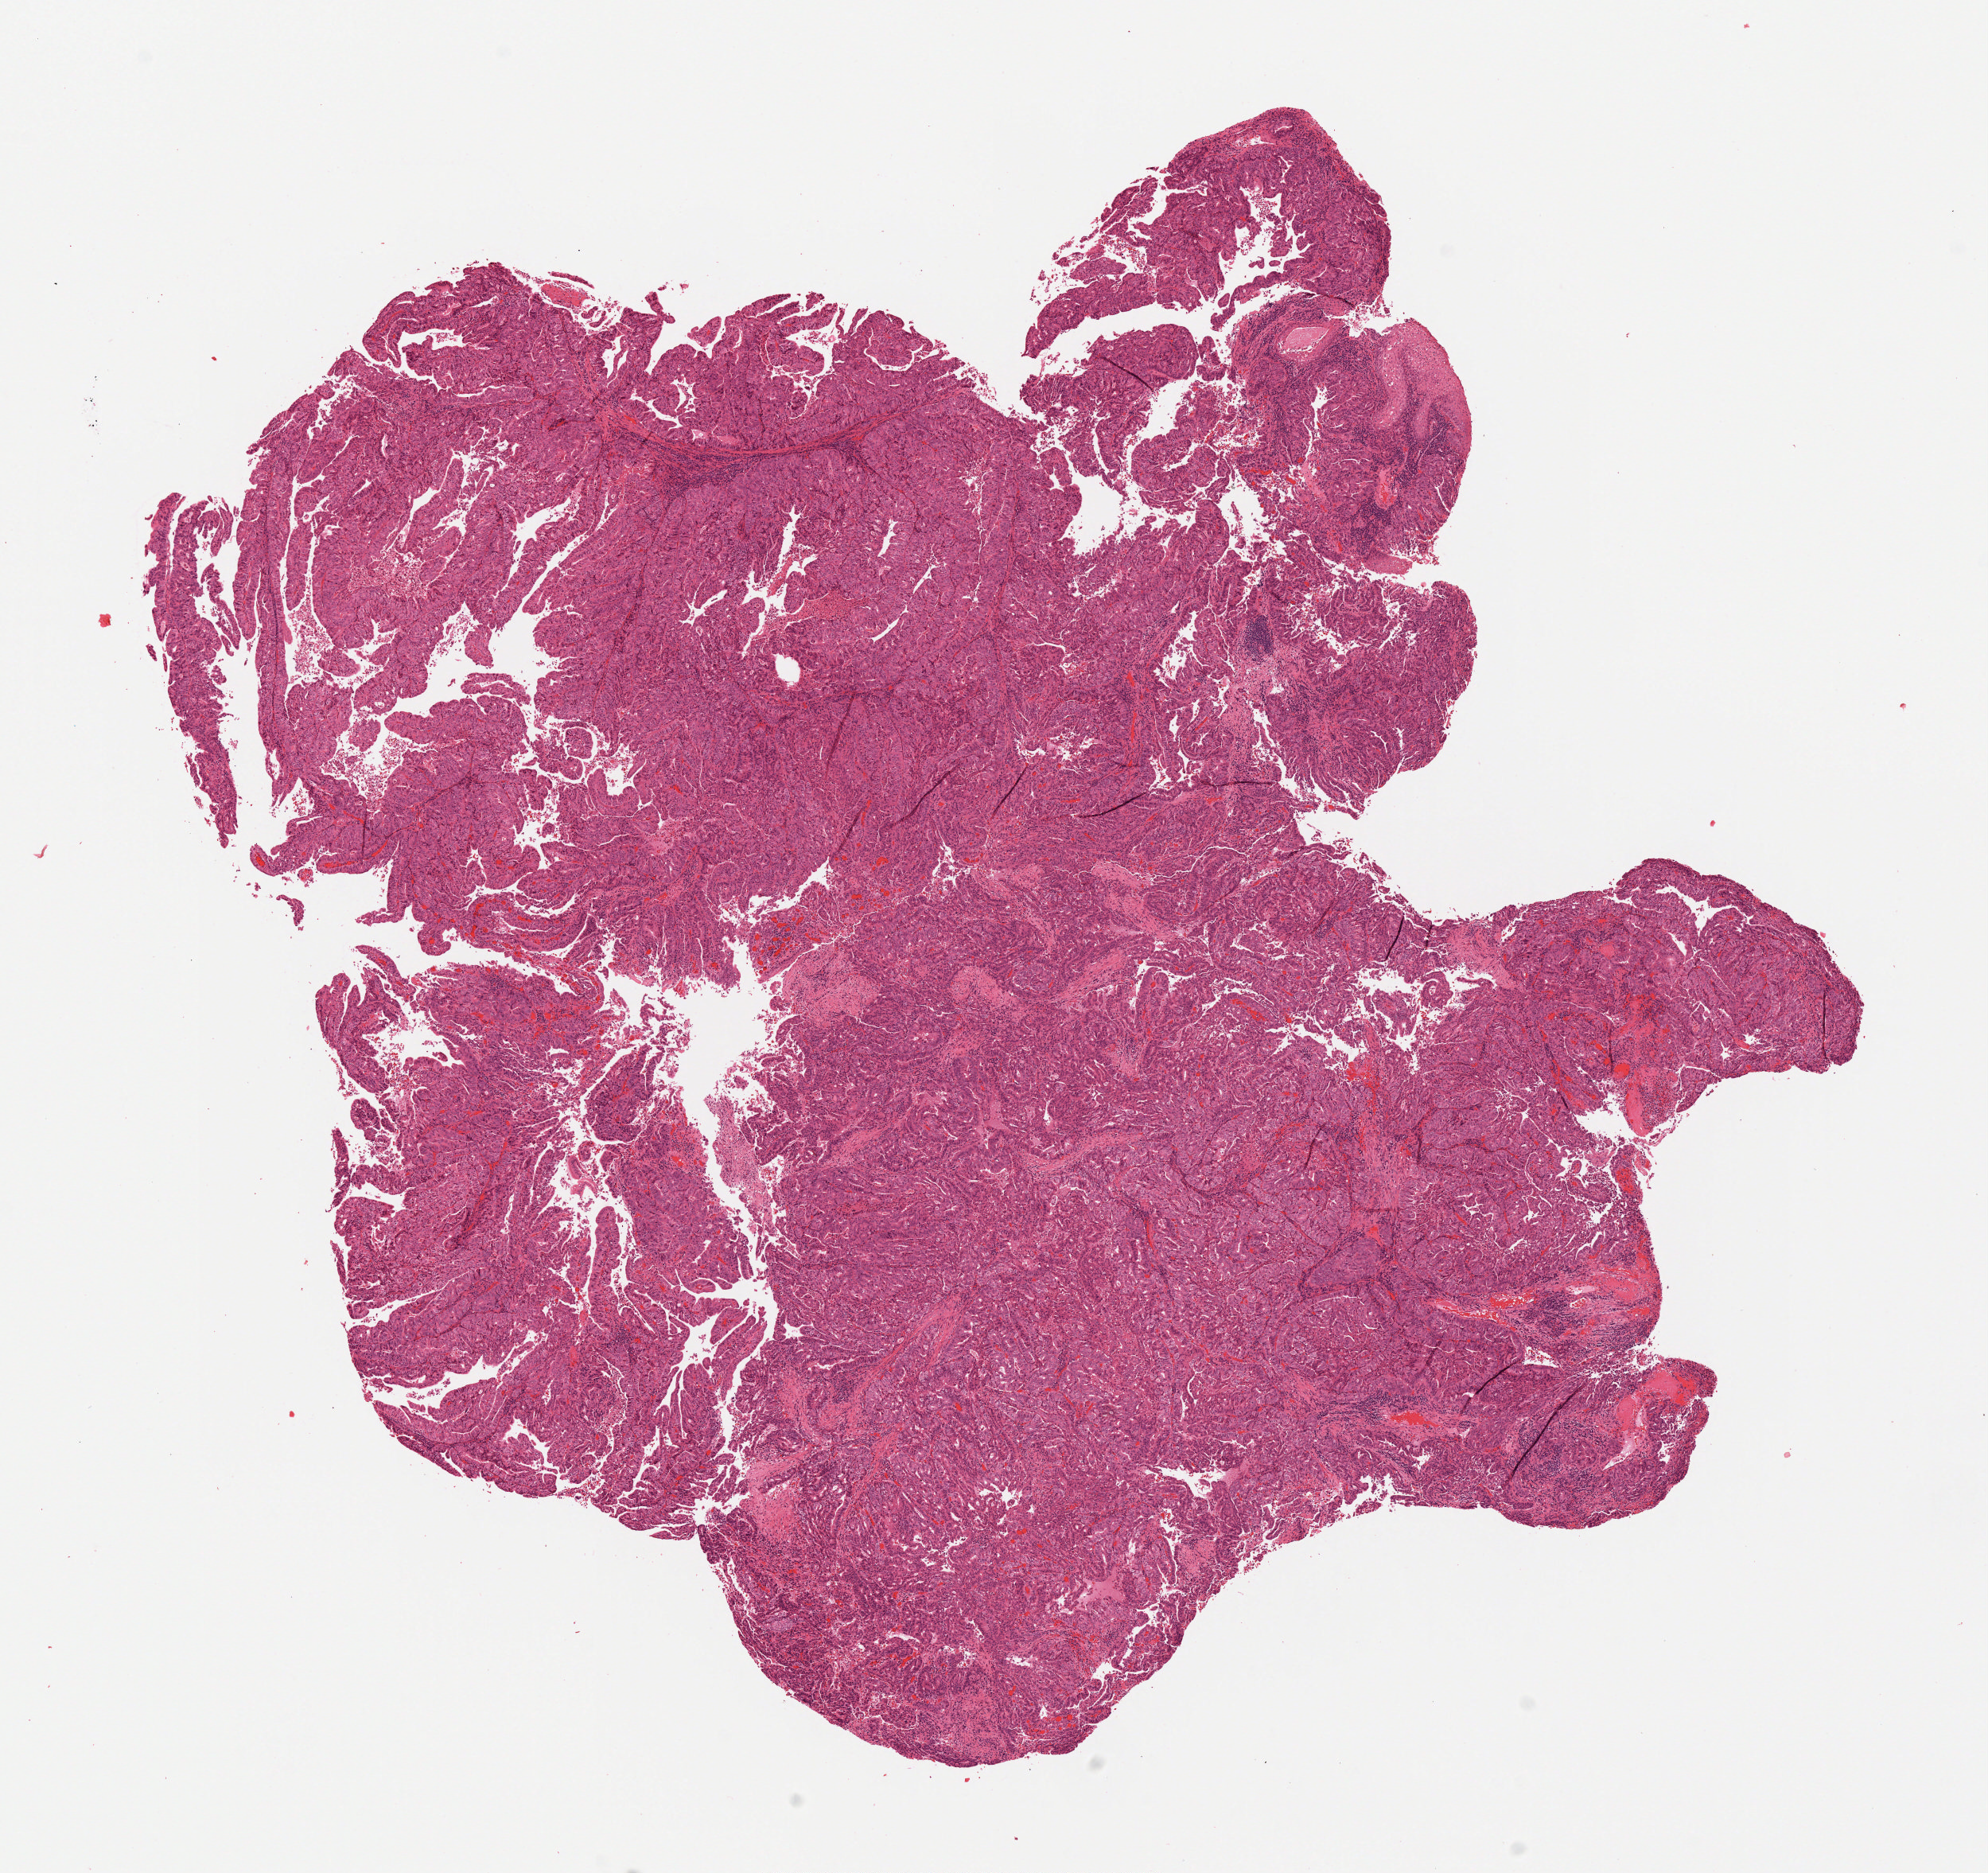
H&E whole-slide image — shown as a low-resolution overview of the whole scanned area (about 10.0 x 9.4 mm, acquisition: 20x scan); formalin-fixed paraffin-embedded (FFPE) diagnostic section; primary tumour sample from the esophagus. Patient: male, age at initial diagnosis 58 years. Histologic grade: G2 (moderately differentiated).
* pathologic diagnosis: Adenocarcinoma, NOS
* TNM: T3 N0 M0
* AJCC pathologic stage: IIA